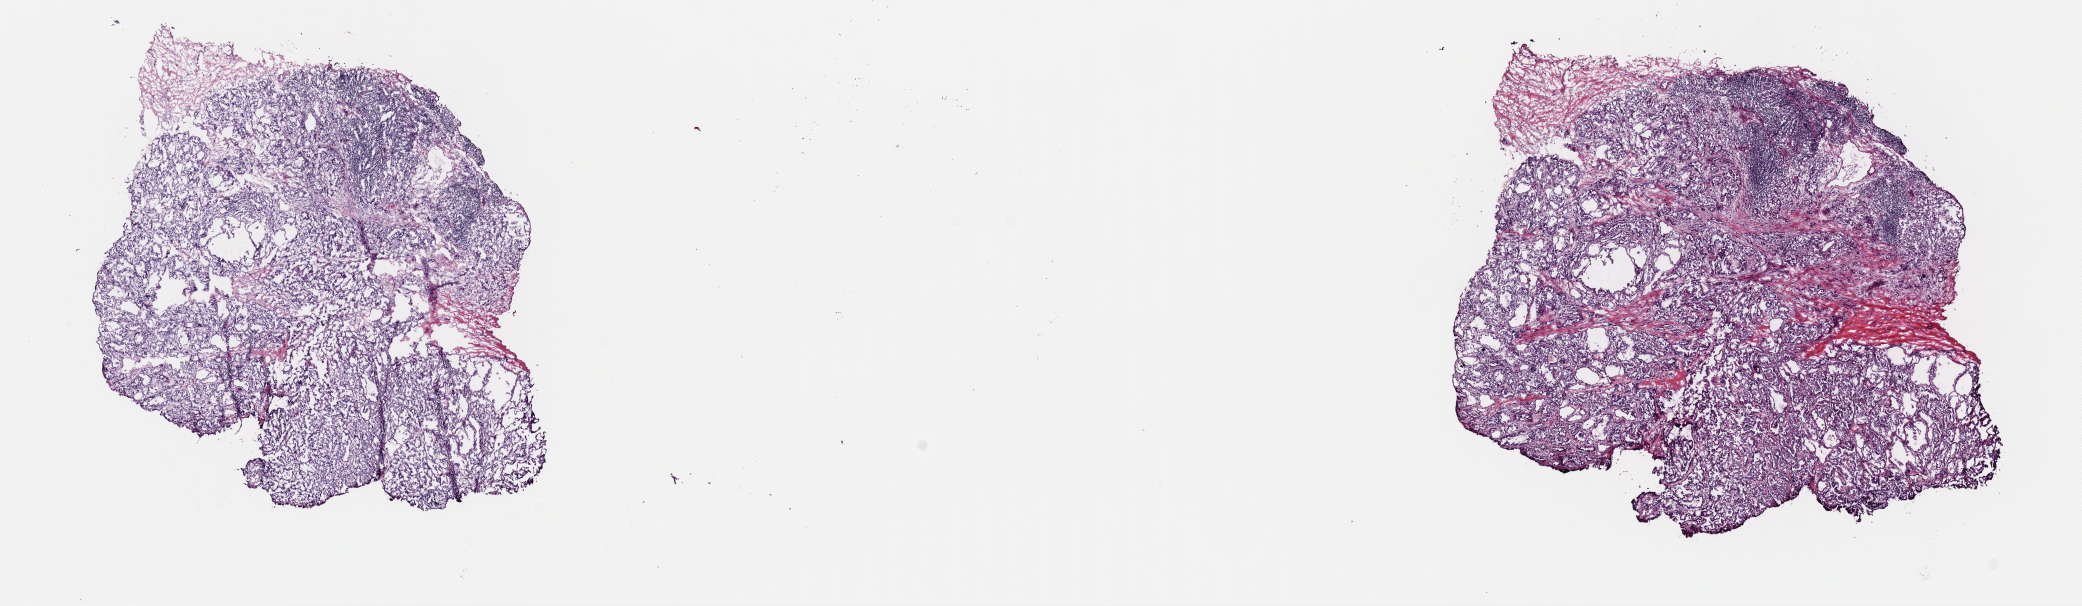
Digitized H&E-stained tissue section (whole slide), a low-resolution overview of the entire scanned area, about 16.4 x 4.8 mm, frozen section from the top of the tissue portion, sample: primary tumour, thyroid. Female, age 51 years at initial diagnosis. Pathologist review of this section (percent, as recorded): tumour cells 85%, tumour nuclei 85%, normal cells 5%, stromal cells 10%, necrosis 0%. Infiltration values recorded for this section: lymphocyte infiltration 1%, monocyte infiltration 1%, neutrophil infiltration 0%.
- histologic diagnosis: Papillary carcinoma, oxyphilic cell (thyroid gland)
- lymph nodes positive (case pathology): 35 of 49 examined
- AJCC pathologic stage: IVA (7th edition)